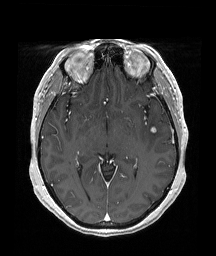
Brain MRI from a brain-tumour surgery series, one axial slice. Slice 109 of 192 in the series (ordered by position). T1-weighted post-contrast. 1 mm slice thickness. 216 × 256 image matrix, field of view 211 × 250 mm. Case-level facts recorded for this patient, not image findings: histopathology: Papillary glioneuronal tumor; WHO grade: 1.
Outlined on this slice (outlined manually by an expert reader):
- tumour: box from (x=150, y=127) to (x=156, y=132) px